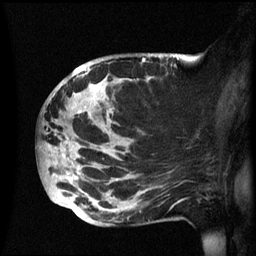
Breast MRI (dynamic contrast-enhanced), one sagittal slice; dynamic contrast-enhanced series, image 2 of 3 at this slice position (ordered by acquisition); 1.5 T; TE 4.2 ms, TR 8.4 ms; 2.4 mm slice thickness; 256 × 256 image matrix, field of view 230 × 230 mm. Patient: female, 49 years.
Outlined on this slice (semi-automatically segmented with operator editing):
- analysis volume of interest (the breast-tissue region the enhancement analysis was run in; not a lesion): bounding box (x1, y1, x2, y2) in pixels: (38, 54, 174, 226)
- tumour enhancement mask (voxels above the 70 % enhancement threshold inside the analysis volume of interest): (78, 69, 151, 114)